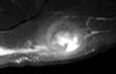
MRI of an extremity soft-tissue mass, one axial slice; slice 23 of 36 in the series (ordered by position); STIR; MR volume resampled by the dataset authors to the PET/CT grid (not the native acquisition matrix); 3.27 mm slice thickness; 116 × 74 image matrix, field of view 113 × 72 mm. Male patient. Case-level facts recorded for this patient, not image findings: histological type: pleiomorphic leiomyosarcoma; grade: high; site of the primary tumour: left buttock.
Structures marked on this image (expert contour drawn on MRI and transferred to this co-registered scan by the dataset authors):
- gross tumour volume including surrounding oedema: bounding box [x1, y1, x2, y2] px = [37, 21, 79, 56]
- gross tumour volume (mass): [39, 21, 79, 56]